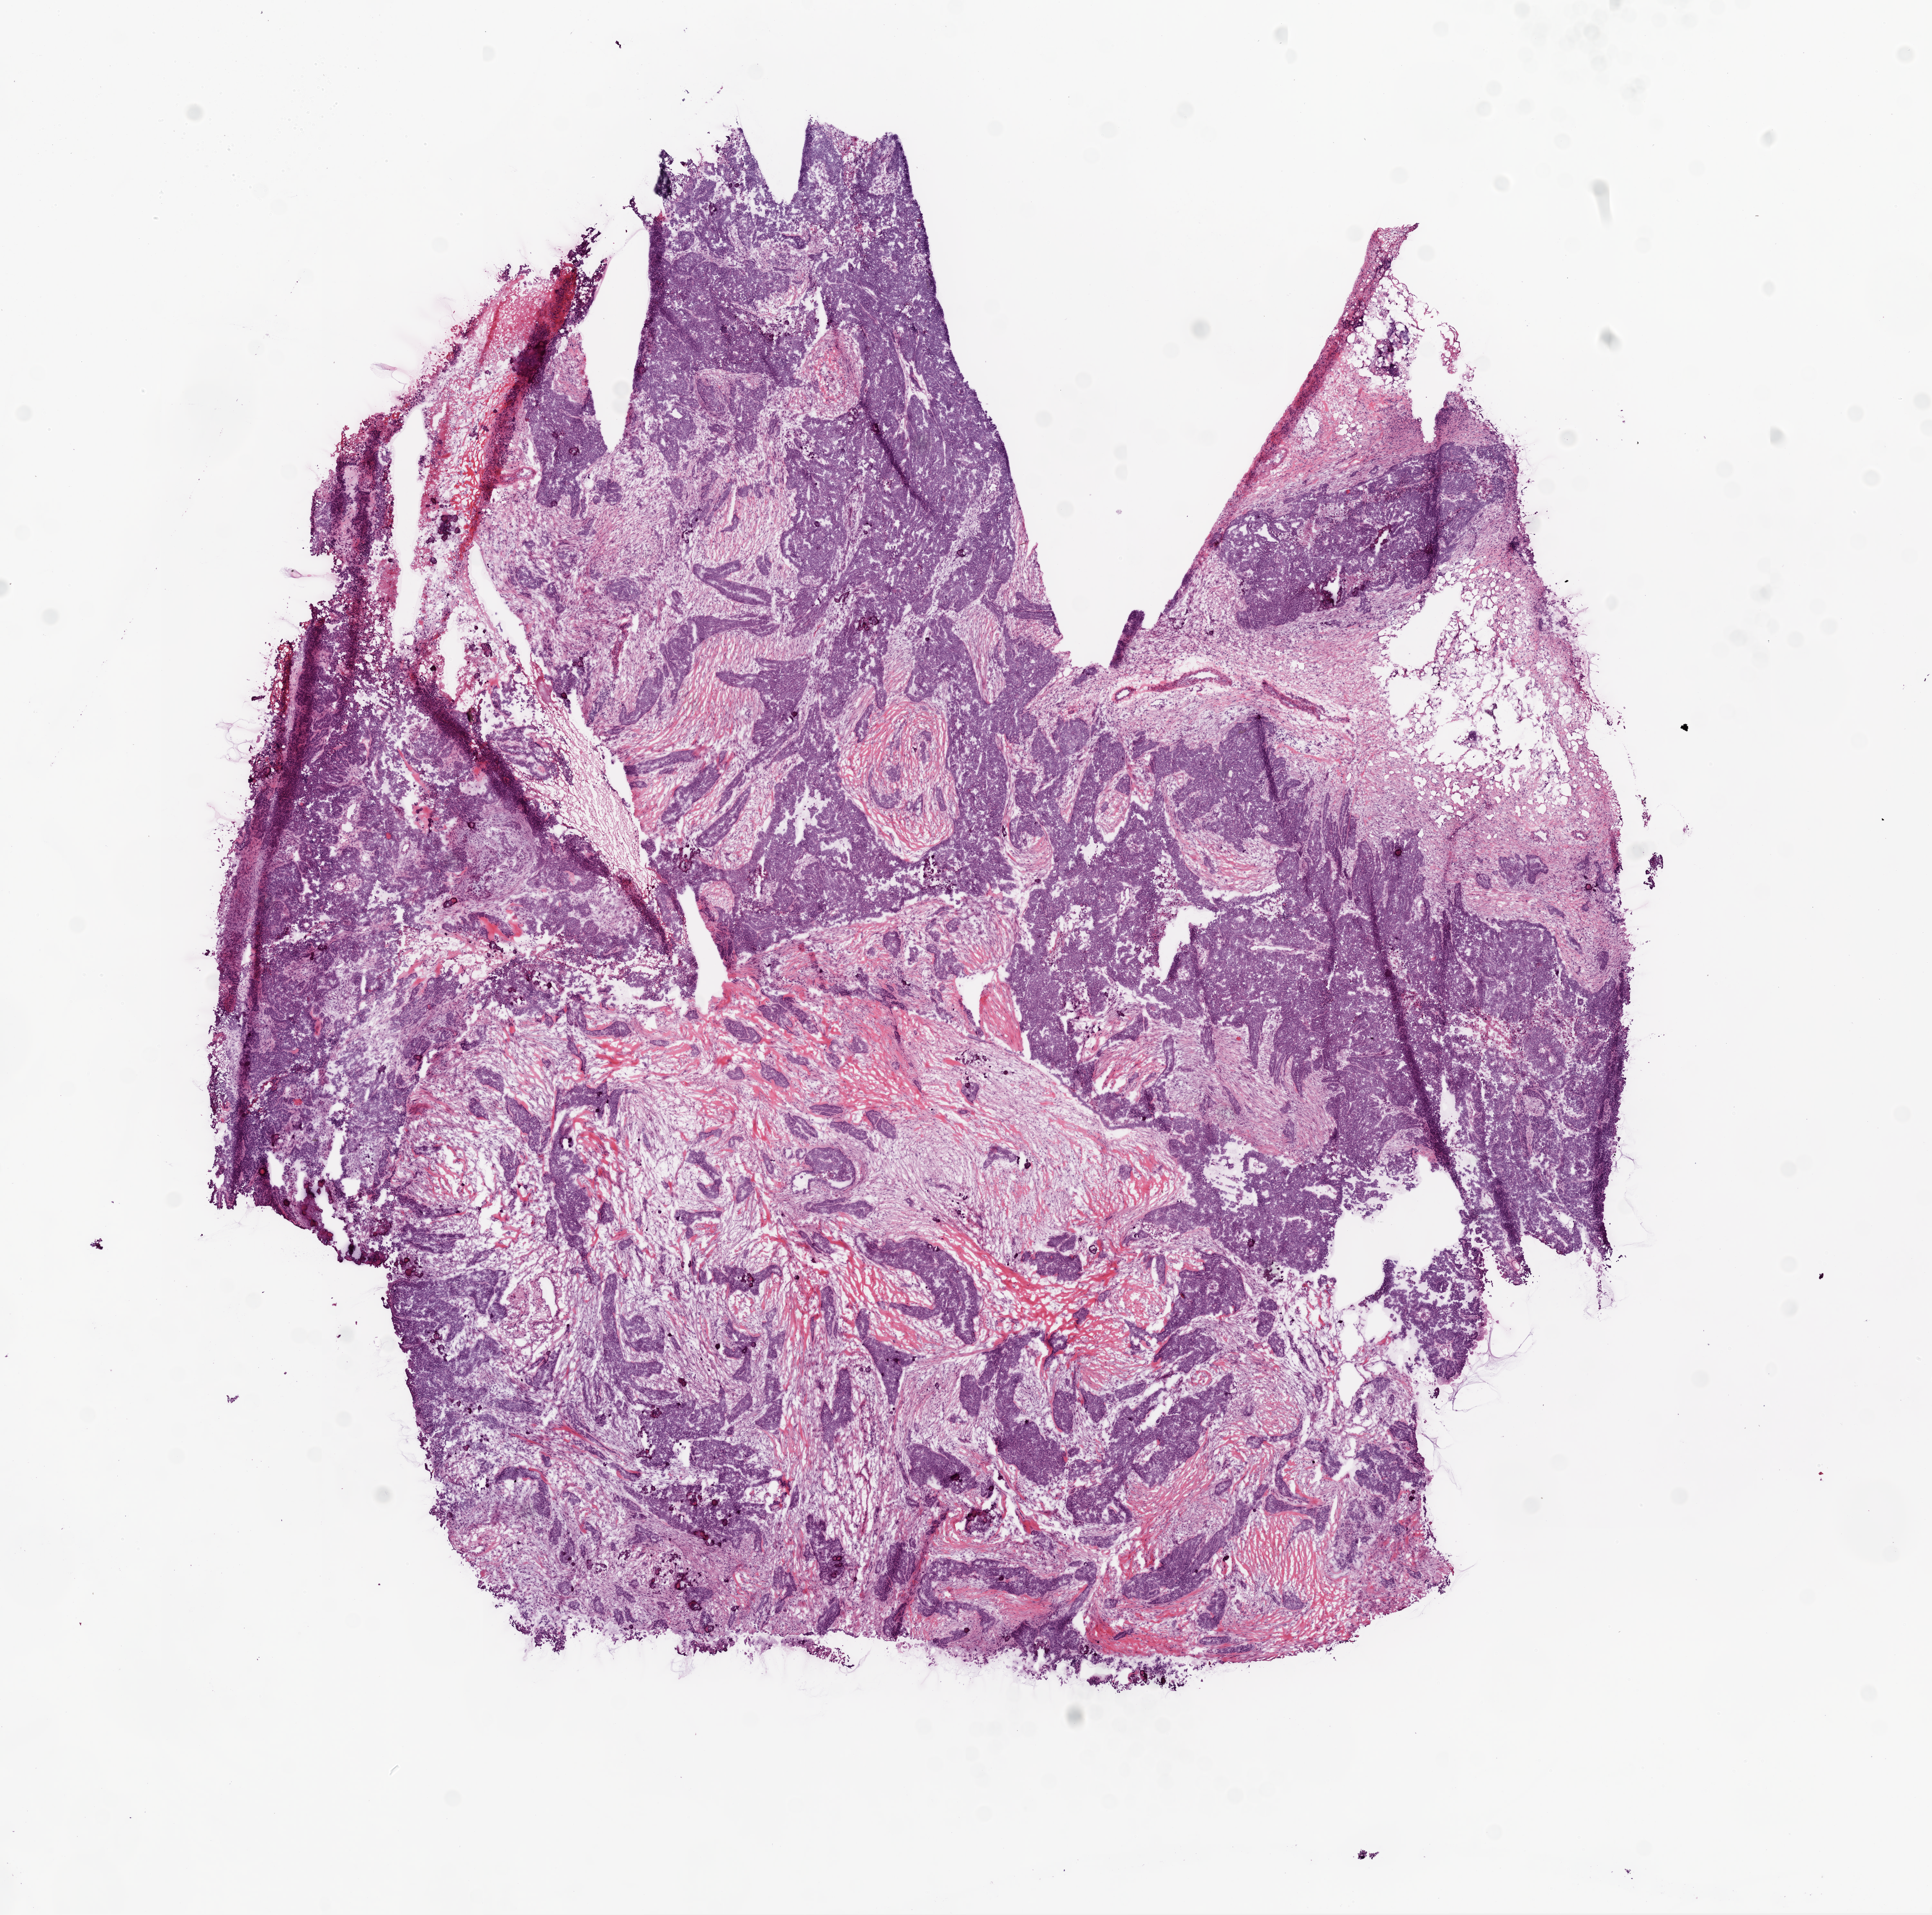
Digitized H&E-stained tissue section (whole slide) — whole scanned area (about 12.0 x 11.9 mm, slide scanned at 20x) shown as a low-resolution overview, frozen section, ovary, primary tumour sample. Female, age 75 years at initial diagnosis. Histologic grade: G2 (moderately differentiated). Pathologist review of this section (percent, as recorded): tumour cells 60%, tumour nuclei 76%, normal cells 35%, stromal cells 0%, necrosis 5%.
* FIGO stage: IIIC
* histologic diagnosis: Serous cystadenocarcinoma, NOS